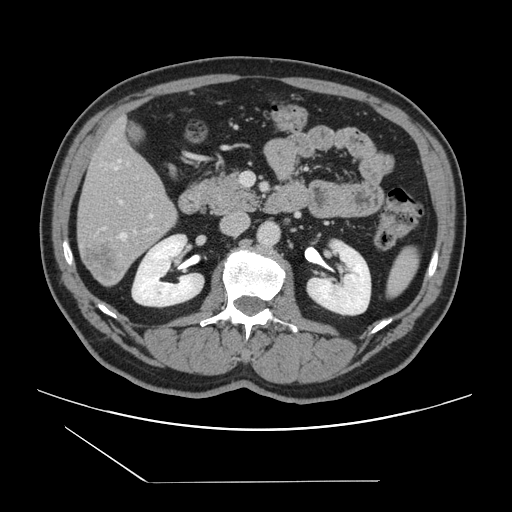
Contrast-enhanced abdominal CT, one axial slice. Slice 59 of 157 in the series (ordered by position). 120 kVp. Intravenous contrast given. Soft-tissue window (W 400 / L 40 HU). 2.5 mm slice thickness. 512 × 512 image matrix, field of view 407 × 407 mm. Male patient, age 61 years. From the clinical record (not read from this slice): diagnosis: colorectal cancer liver metastases, imaged before liver resection; multiple liver metastases: yes.
Outlined on this slice (outlined manually by an expert reader):
- hepatic veins: bounding box <116,160,135,239> (left, top, right, bottom; pixels)
- liver: <78,122,177,286>
- planned liver remnant (the part of the liver to remain after resection): <79,122,169,218>
- portal vein (with intrahepatic branches): <103,200,153,228>
- liver metastasis: <82,242,128,284>